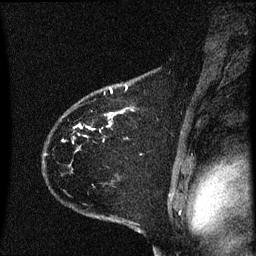
Breast MRI (dynamic contrast-enhanced), one sagittal slice; slice 49 of 60 in the series (ordered by position); dynamic contrast-enhanced series, image 2 of 3 at this slice position (ordered by acquisition); 1.5 T; TE 4.2 ms, TR 8.4 ms; 2 mm slice thickness; 256 × 256 image matrix, field of view 200 × 200 mm. Patient: female, 35 years. Case-level facts recorded for this patient, not image findings: setting: breast cancer imaged before/during neoadjuvant chemotherapy; receptor status: HER2-positive.
Structures marked on this image (semi-automatic segmentation, software-assisted and operator-edited):
- analysis volume of interest (the breast-tissue region the enhancement analysis was run in; not a lesion): bounding box <45,68,174,173> (left, top, right, bottom; pixels)
- tumour enhancement mask (voxels above the 70 % enhancement threshold inside the analysis volume of interest): <80,86,127,127>